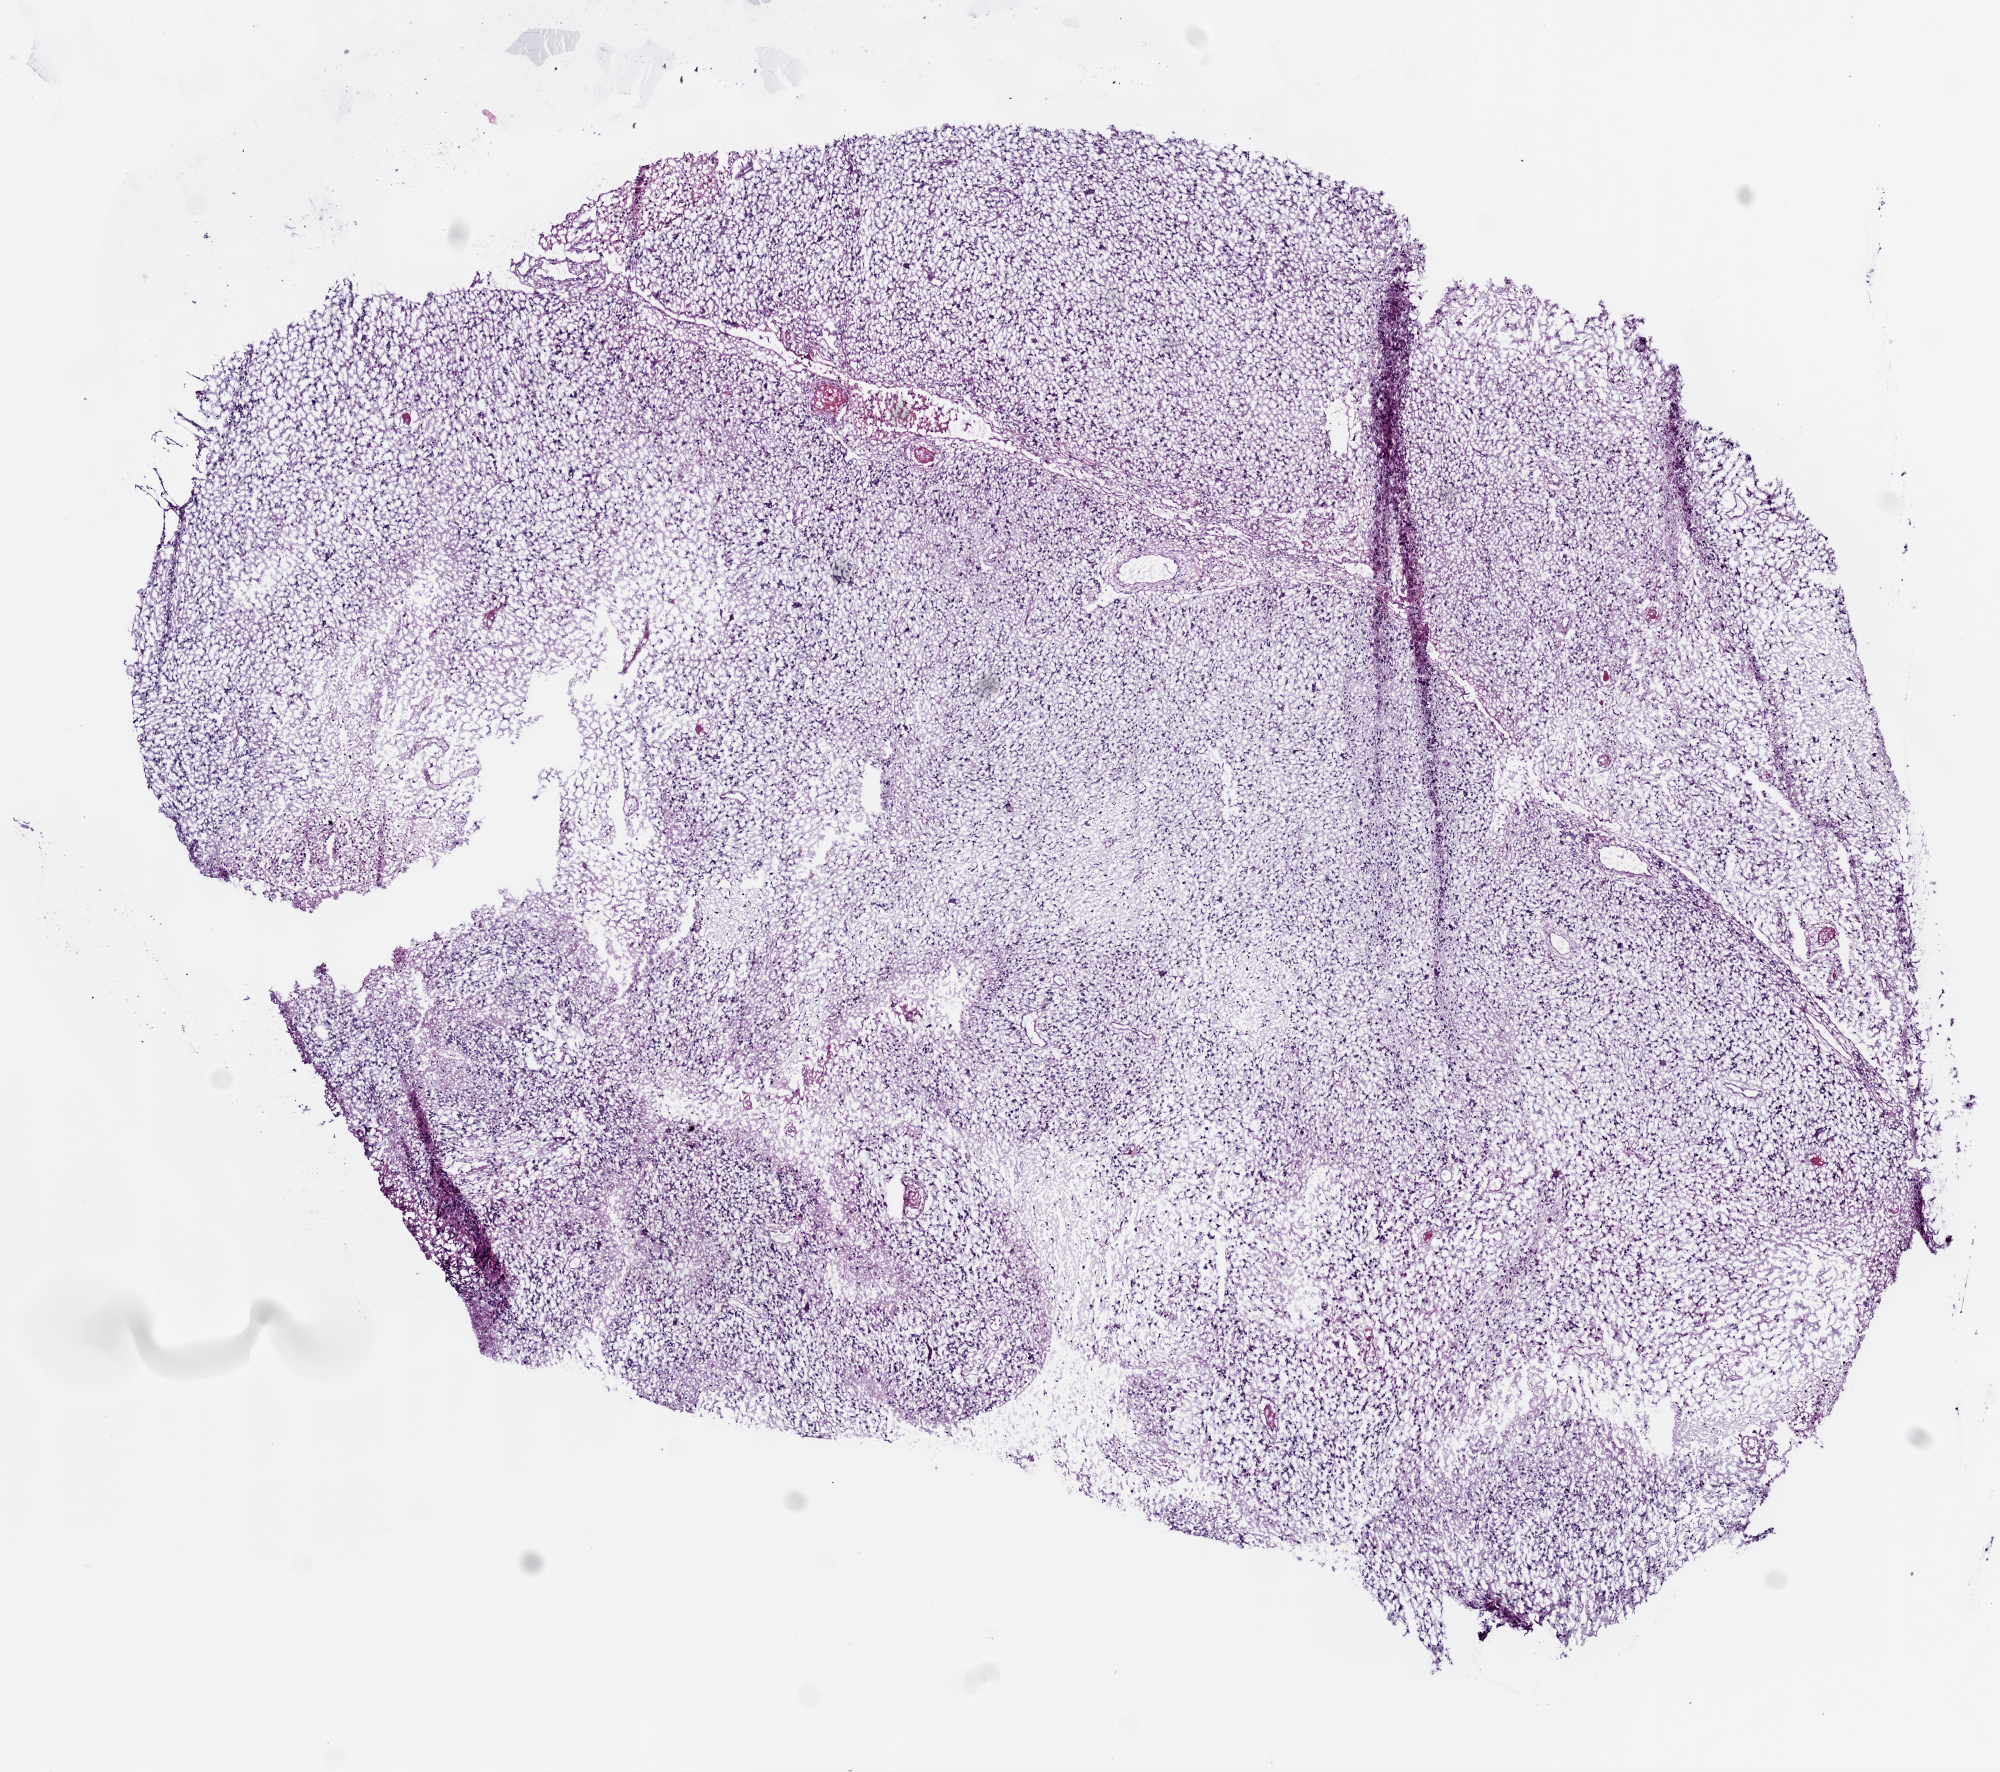
Digitized H&E tissue section (whole slide), whole scanned area (about 8.0 x 7.1 mm, acquisition: 20x scan) shown as a low-resolution overview, frozen section from the bottom of the tissue portion, primary tumour sample from the brain. Male, age 52 years at initial diagnosis. Pathologist review of this section (percent, as recorded): tumour cells 95%, tumour nuclei 75%.
Pathologic diagnosis: Glioblastoma.